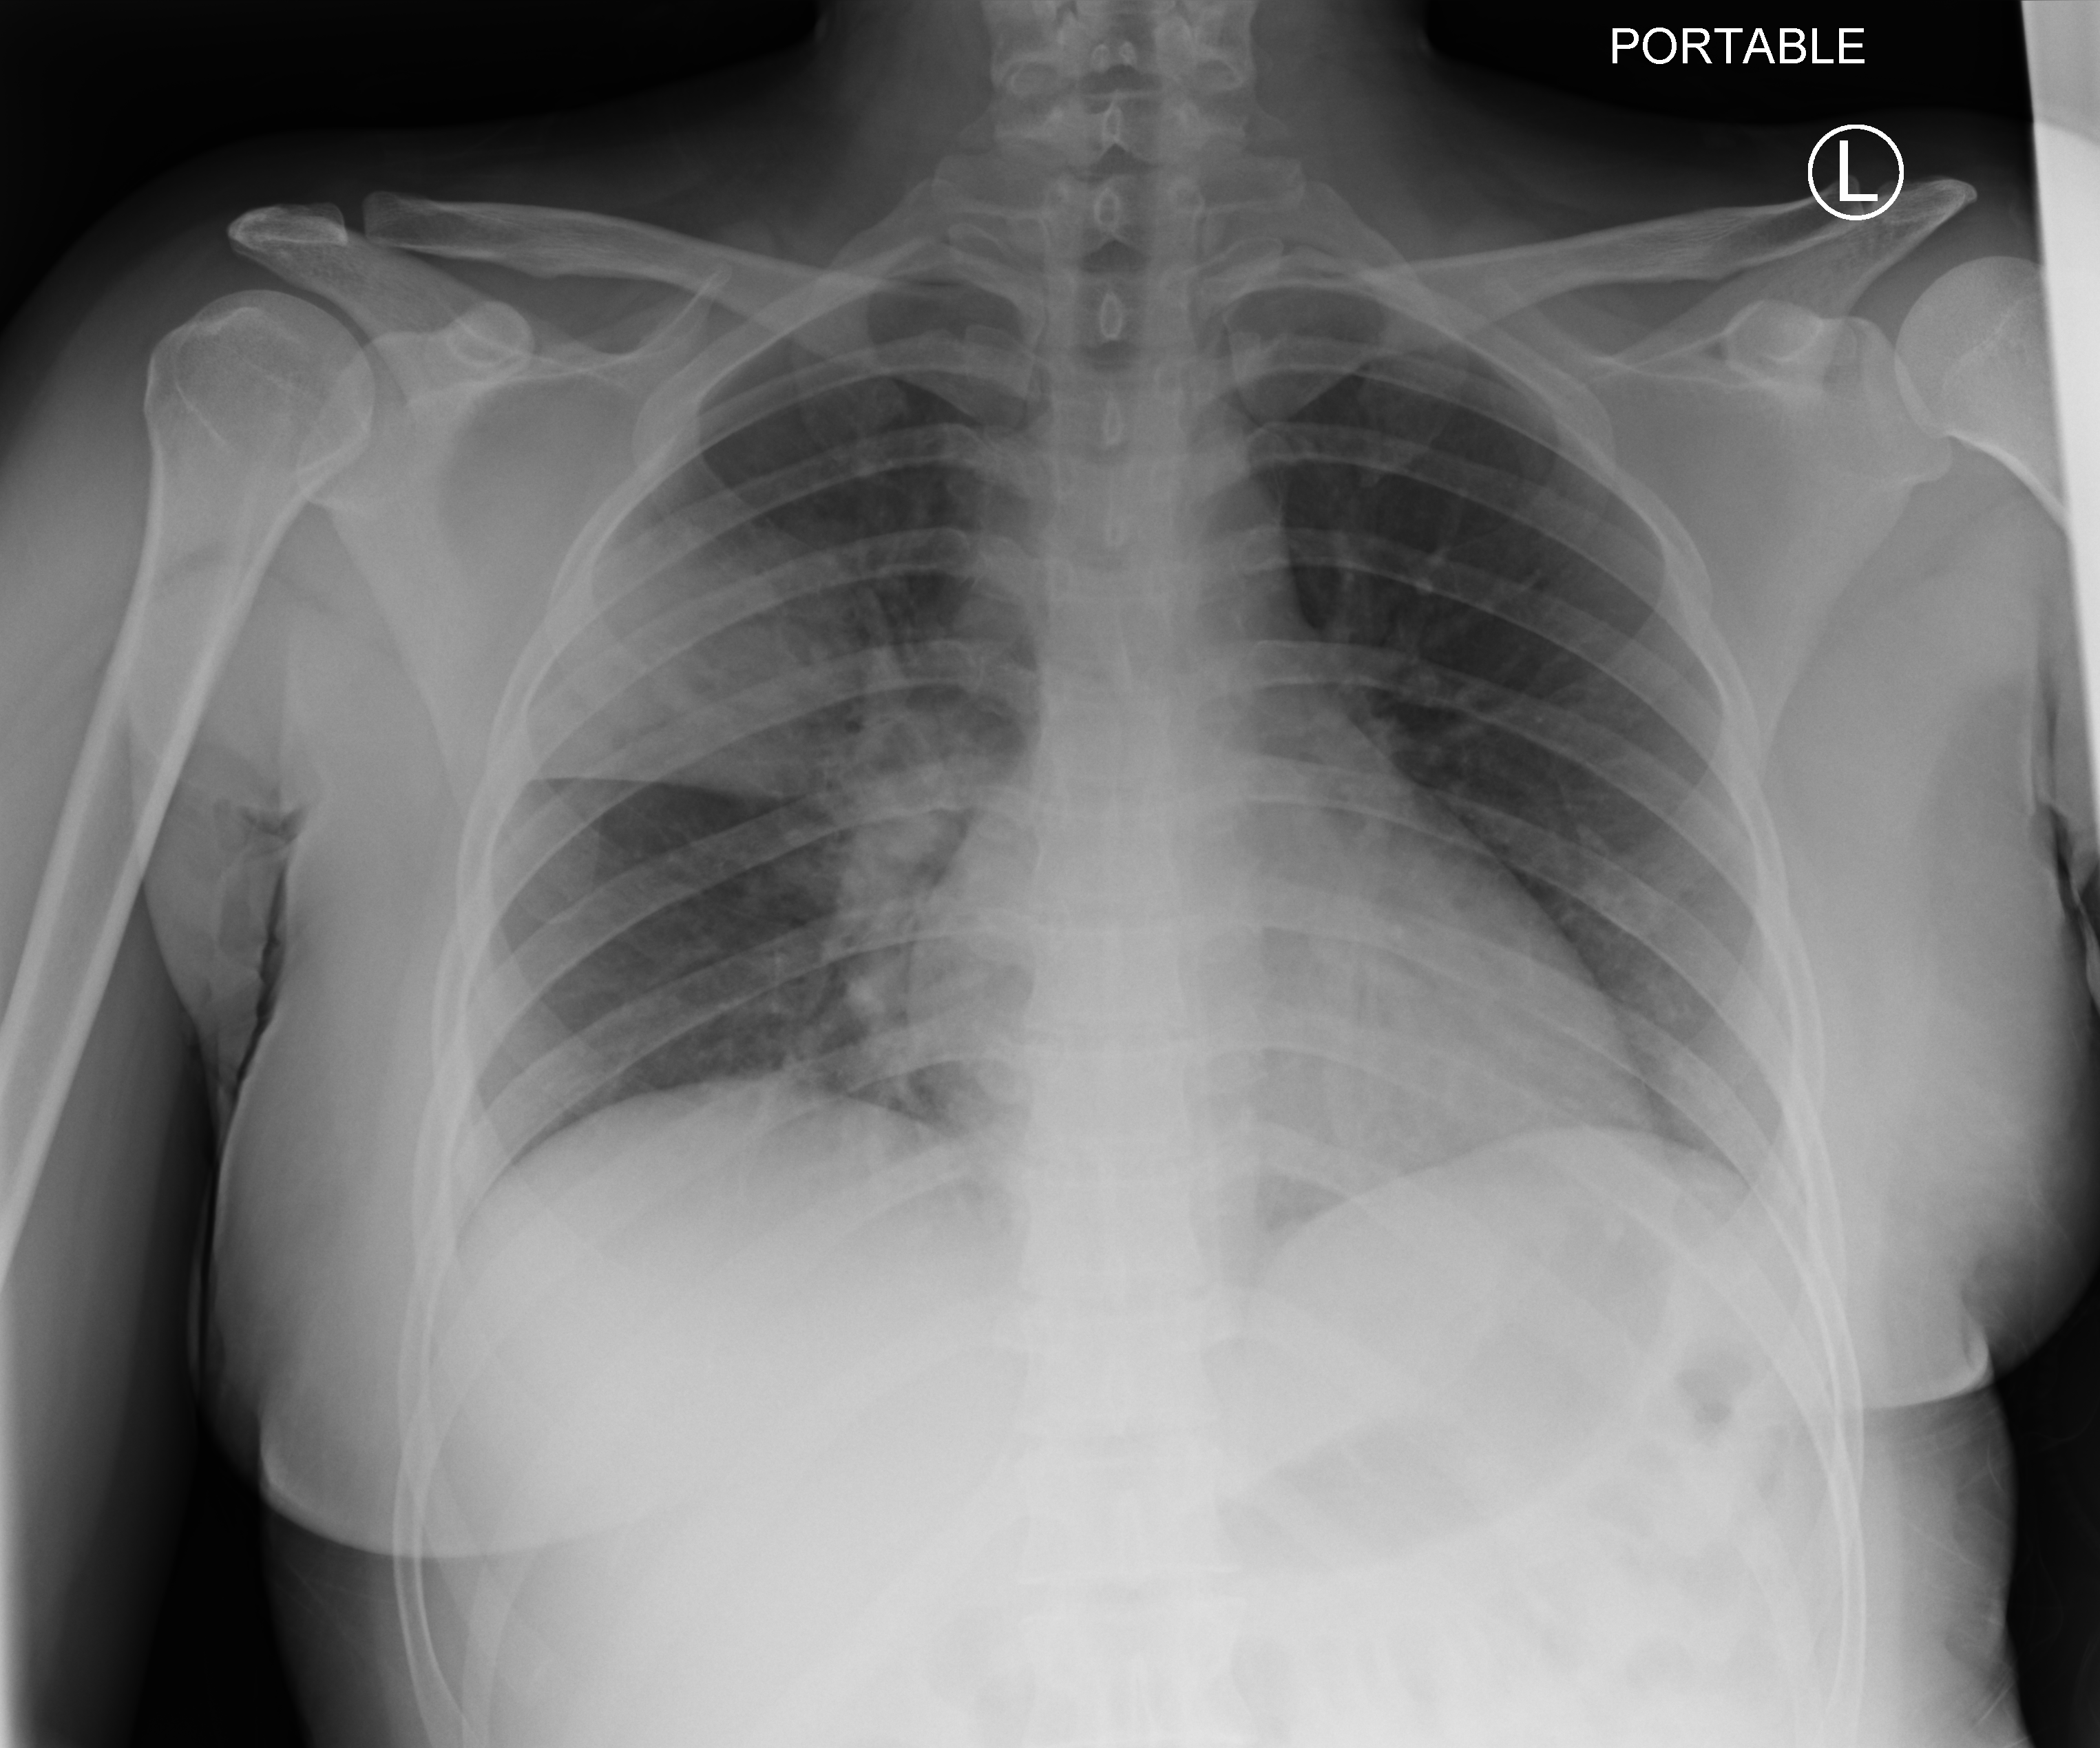
Portable chest radiograph; anteroposterior (AP) projection. Female patient hospitalised with COVID-19, age 18–59 years.
From the hospital-stay record, not from the radiograph (when in the stay this image was taken is not recorded):
- length of hospital stay: 1 day